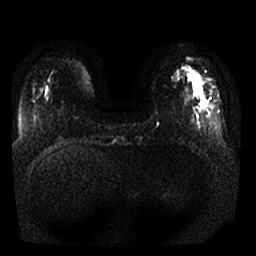
Breast MRI, one axial slice. Position 5 of 25 along the scan axis. Diffusion-weighted series; image 2 of 4 stored at this slice position (different b-values; order by instance number). 1.5 T. 4 mm slice thickness. 256 × 256 image matrix, field of view 330 × 330 mm. Female patient.
Annotated regions visible in this slice (outlined manually by an expert reader):
- tumour on diffusion-weighted imaging: box from (x=201, y=88) to (x=207, y=107) px